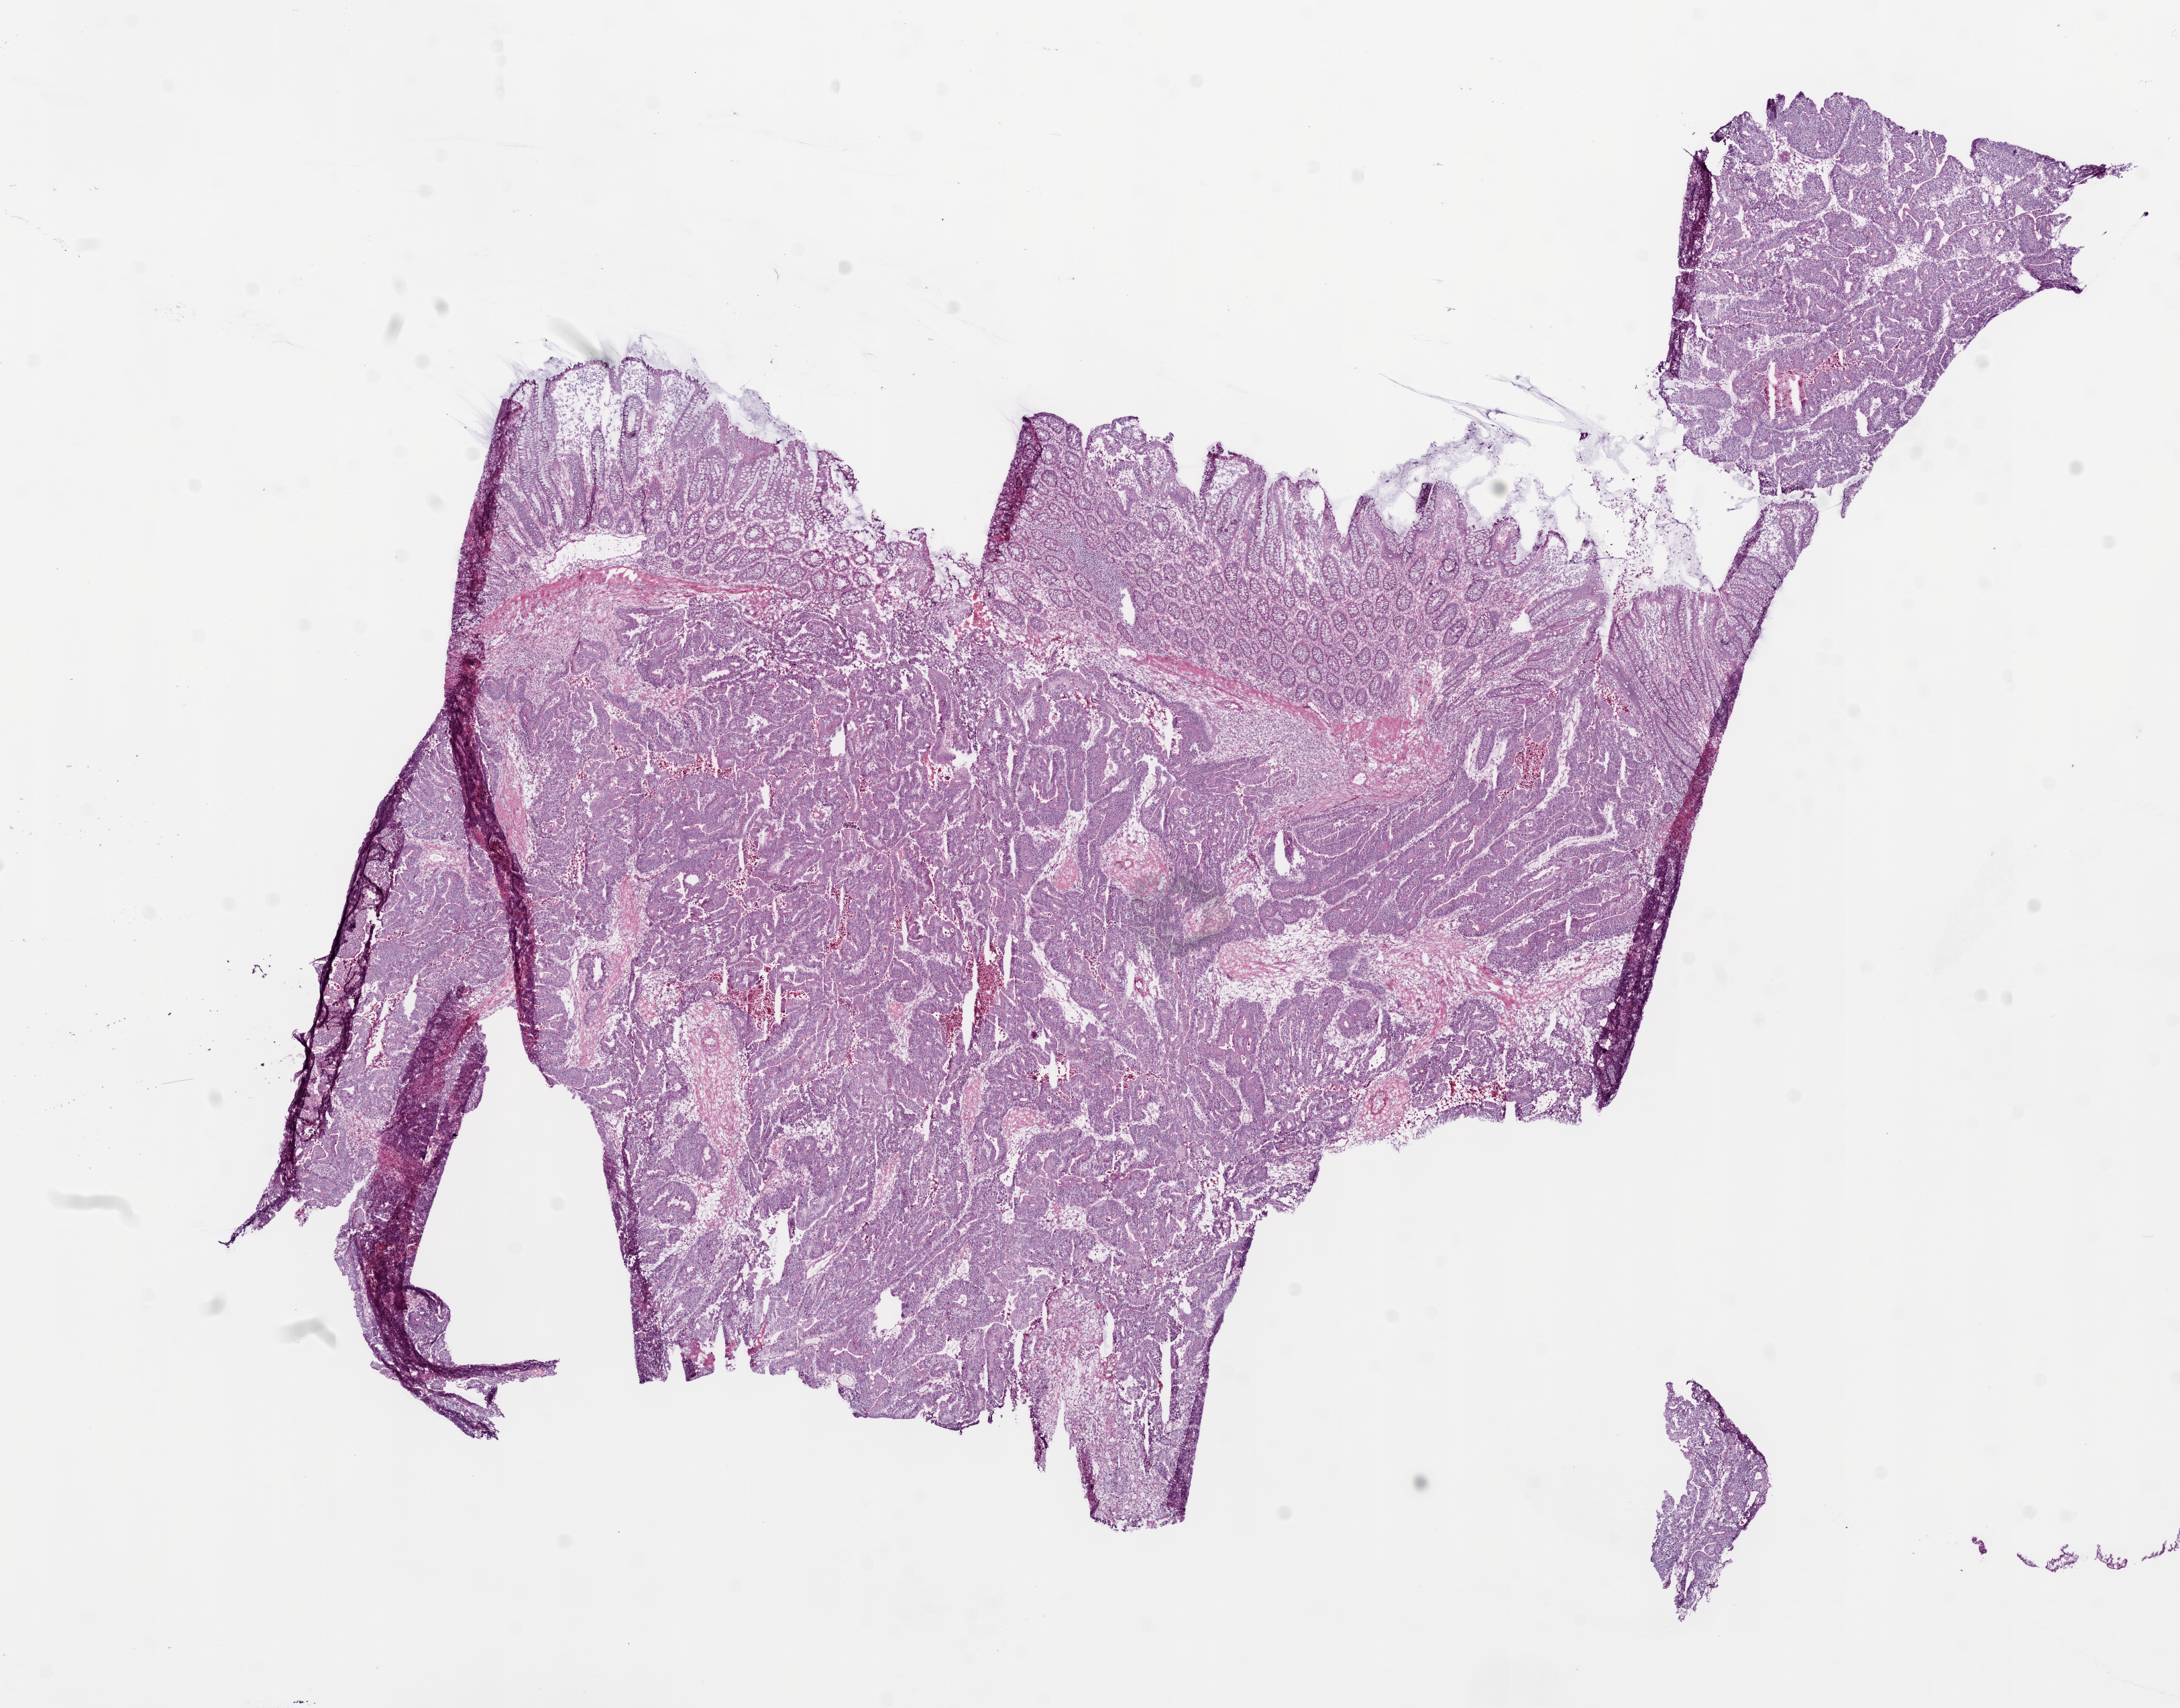
Digitized H&E-stained tissue section (whole slide) — low-resolution overview of the scanned area, about 13.0 x 10.2 mm. Frozen section from the bottom of the tissue portion. Primary tumour sample from the rectum. Female patient; age at initial diagnosis 71 years. Pathologist review of this section (percent, as recorded): tumour cells 72%, tumour nuclei 75%, normal cells 18%, stromal cells 5%, necrosis 5%.
AJCC pathologic stage: IIIB (6th edition). Lymph nodes positive (case pathology): 3 of 19 examined. Histologic diagnosis: Adenocarcinoma, NOS. TNM: T3 N1 M0.